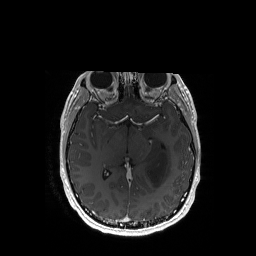
Brain MRI from a brain-tumour surgery series, one axial slice. Position 97 of 192 along the scan axis. T1-weighted post-contrast. 256 × 256 image matrix, field of view 256 × 256 mm. Case-level facts recorded for this patient, not image findings: histopathology: Astrocytoma; WHO grade: 3; IDH mutation: yes.
Structures marked on this image (expert manual segmentation):
- tumour: box from (x=146, y=146) to (x=170, y=187) px